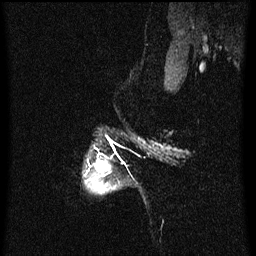
Breast MRI (dynamic contrast-enhanced), one sagittal slice; position 59 of 60 along the scan axis; dynamic contrast-enhanced series, image 2 of 3 at this slice position (ordered by acquisition); 1.5 T; TE 4.2 ms, TR 8 ms; 256 × 256 image matrix, field of view 190 × 190 mm. Patient: female, 50 years.
Annotated regions visible in this slice (semi-automatically segmented with operator editing):
- analysis volume of interest (the breast-tissue region the enhancement analysis was run in; not a lesion): bounding box [x1, y1, x2, y2] px = [85, 160, 115, 194]
- tumour enhancement mask (voxels above the 70 % enhancement threshold inside the analysis volume of interest): [85, 160, 110, 182]